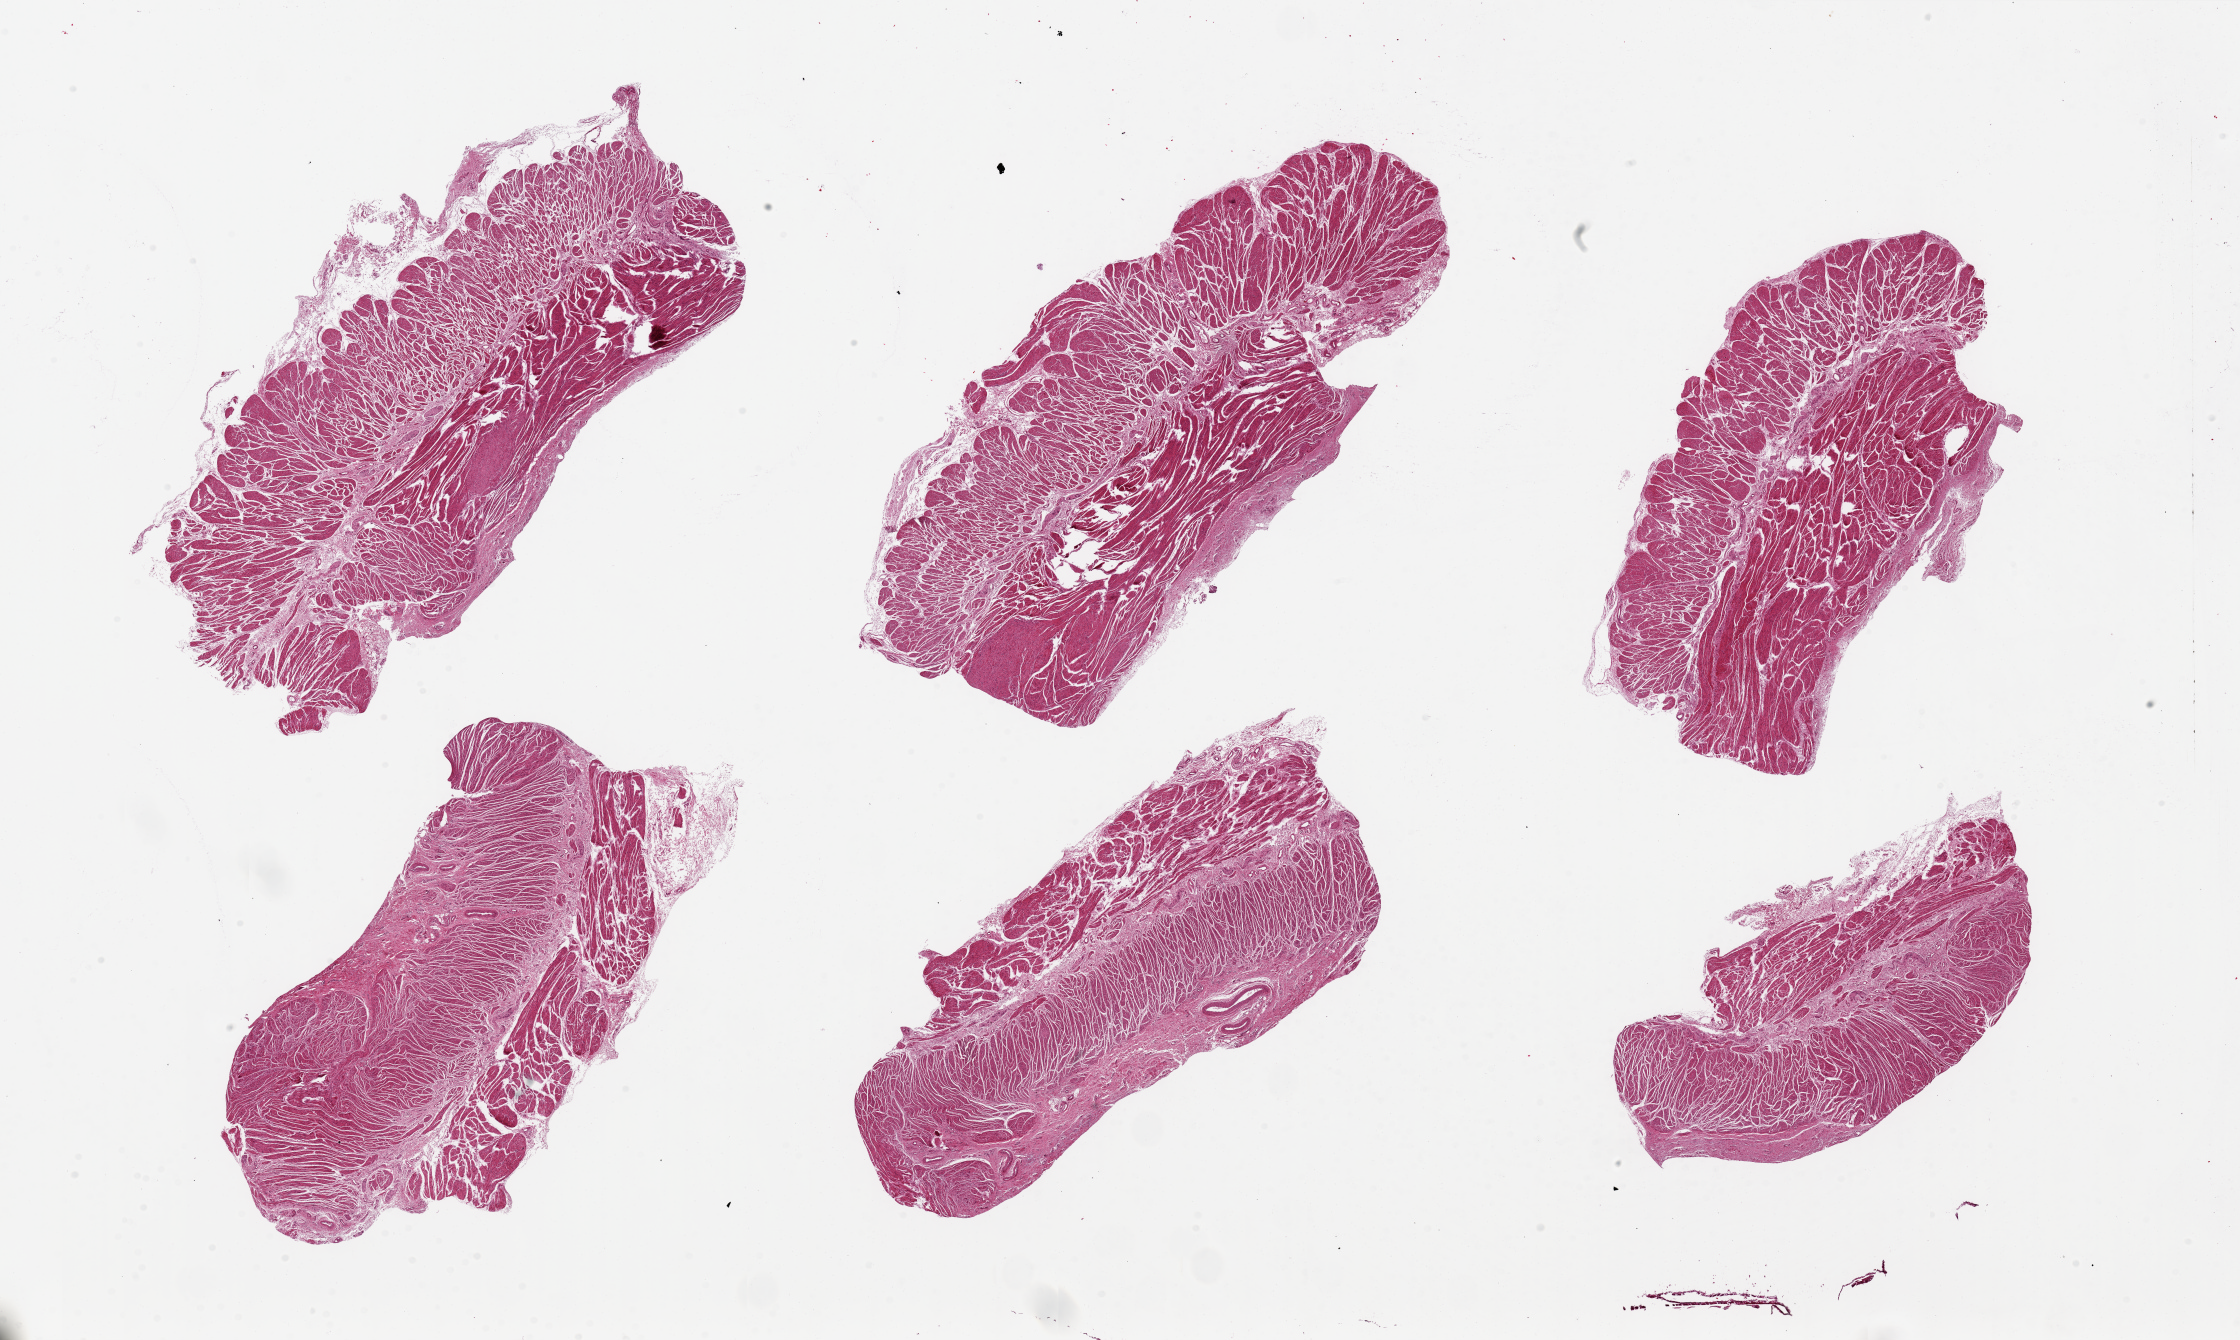
Digitized H&E-stained section, shown as a low-resolution overview of the whole scanned area (about 35.4 x 21.2 mm); PAXgene-fixed, paraffin-embedded tissue; section of gastroesophageal junction (target tissue); tissue donor sample. Female donor.
Reviewer comment on this tissue sample: 6 pieces, up to 12x6mm; all muscularis, good specimens.